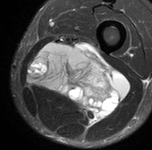
MRI of an extremity soft-tissue mass, one axial slice. Slice 39 of 90 in the series (ordered by position). STIR. MR volume resampled by the dataset authors to the PET/CT grid (not the native acquisition matrix). 3.27 mm slice thickness. 152 × 150 image matrix. Male patient. Case-level facts recorded for this patient, not image findings: histological type: undifferentiated pleomorphic liposarcoma; grade: high; site of the primary tumour: left thigh.
Annotated regions visible in this slice (expert contour drawn on MRI and transferred to this co-registered scan by the dataset authors):
- gross tumour volume including surrounding oedema: bounding box <29,37,128,124> (left, top, right, bottom; pixels)
- gross tumour volume (mass): <29,44,128,124>